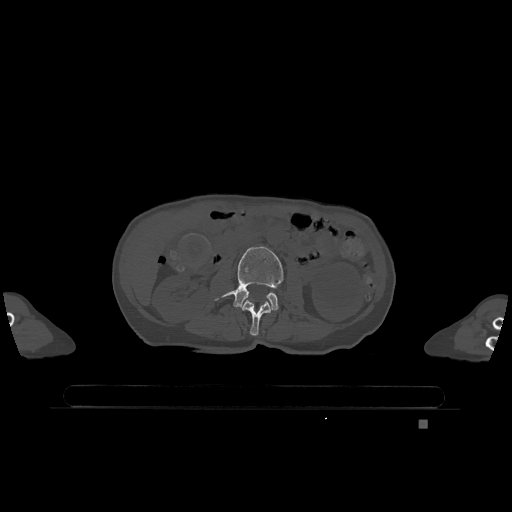
CT including the spine, one axial slice; slice 380 of 1317 in the series (ordered by position); bone window (W 1800 / L 400 HU); 0.5 mm slice thickness; 512 × 512 image matrix, field of view 500 × 500 mm. Female patient, age 74 years. From the clinical record (not read from this slice): primary cancer: lung; vertebrae with lytic lesions (as recorded): T1, T4, T5, T6, L4, L5.
Annotated regions visible in this slice (semi-automatic segmentation, software-assisted and operator-edited):
- L2 vertebra: bounding box <242,300,272,336> (left, top, right, bottom; pixels)
- L3 vertebra: <215,246,284,310>